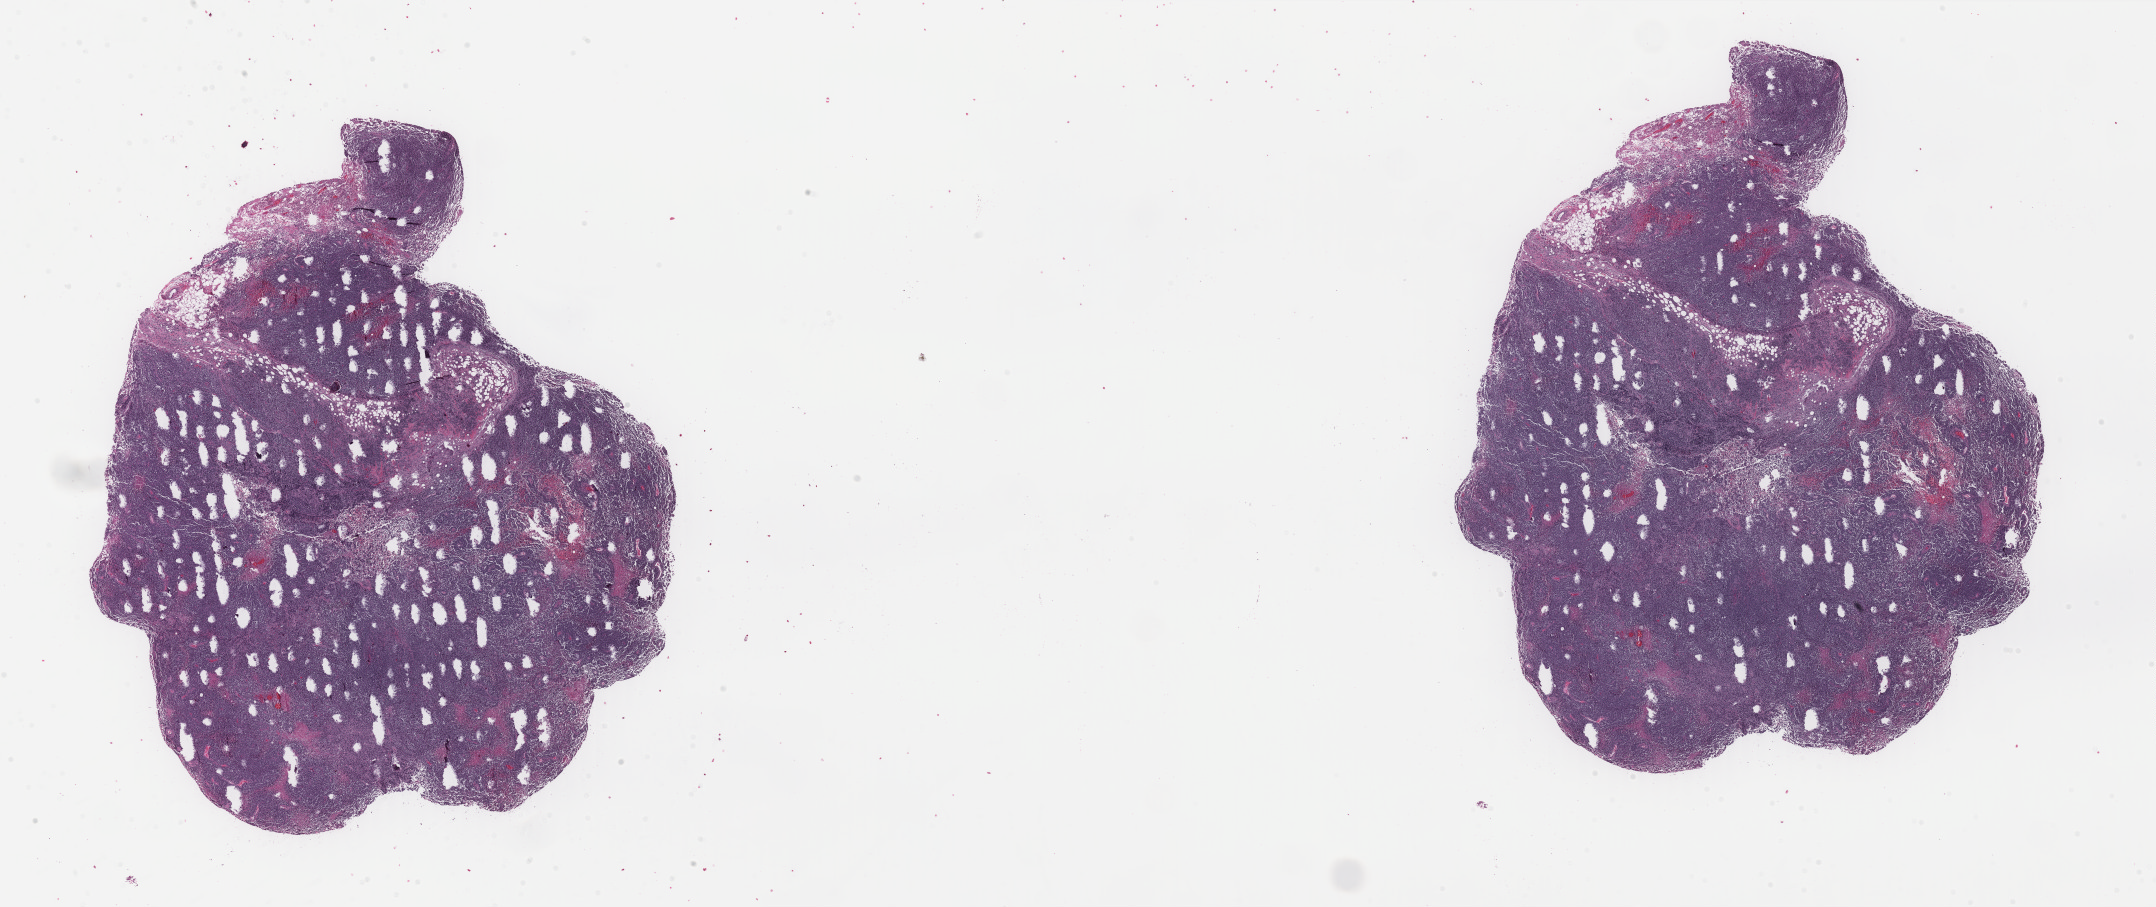
Digitized H&E tissue section (whole slide) — a low-resolution overview of the entire scanned area, about 34.1 x 14.4 mm, formalin-fixed paraffin-embedded (FFPE) diagnostic section, metastatic tumour sample. Patient: female, age at initial diagnosis 34 years.
This section: metastatic tumour tissue. Patient diagnosis: Malignant melanoma, NOS.